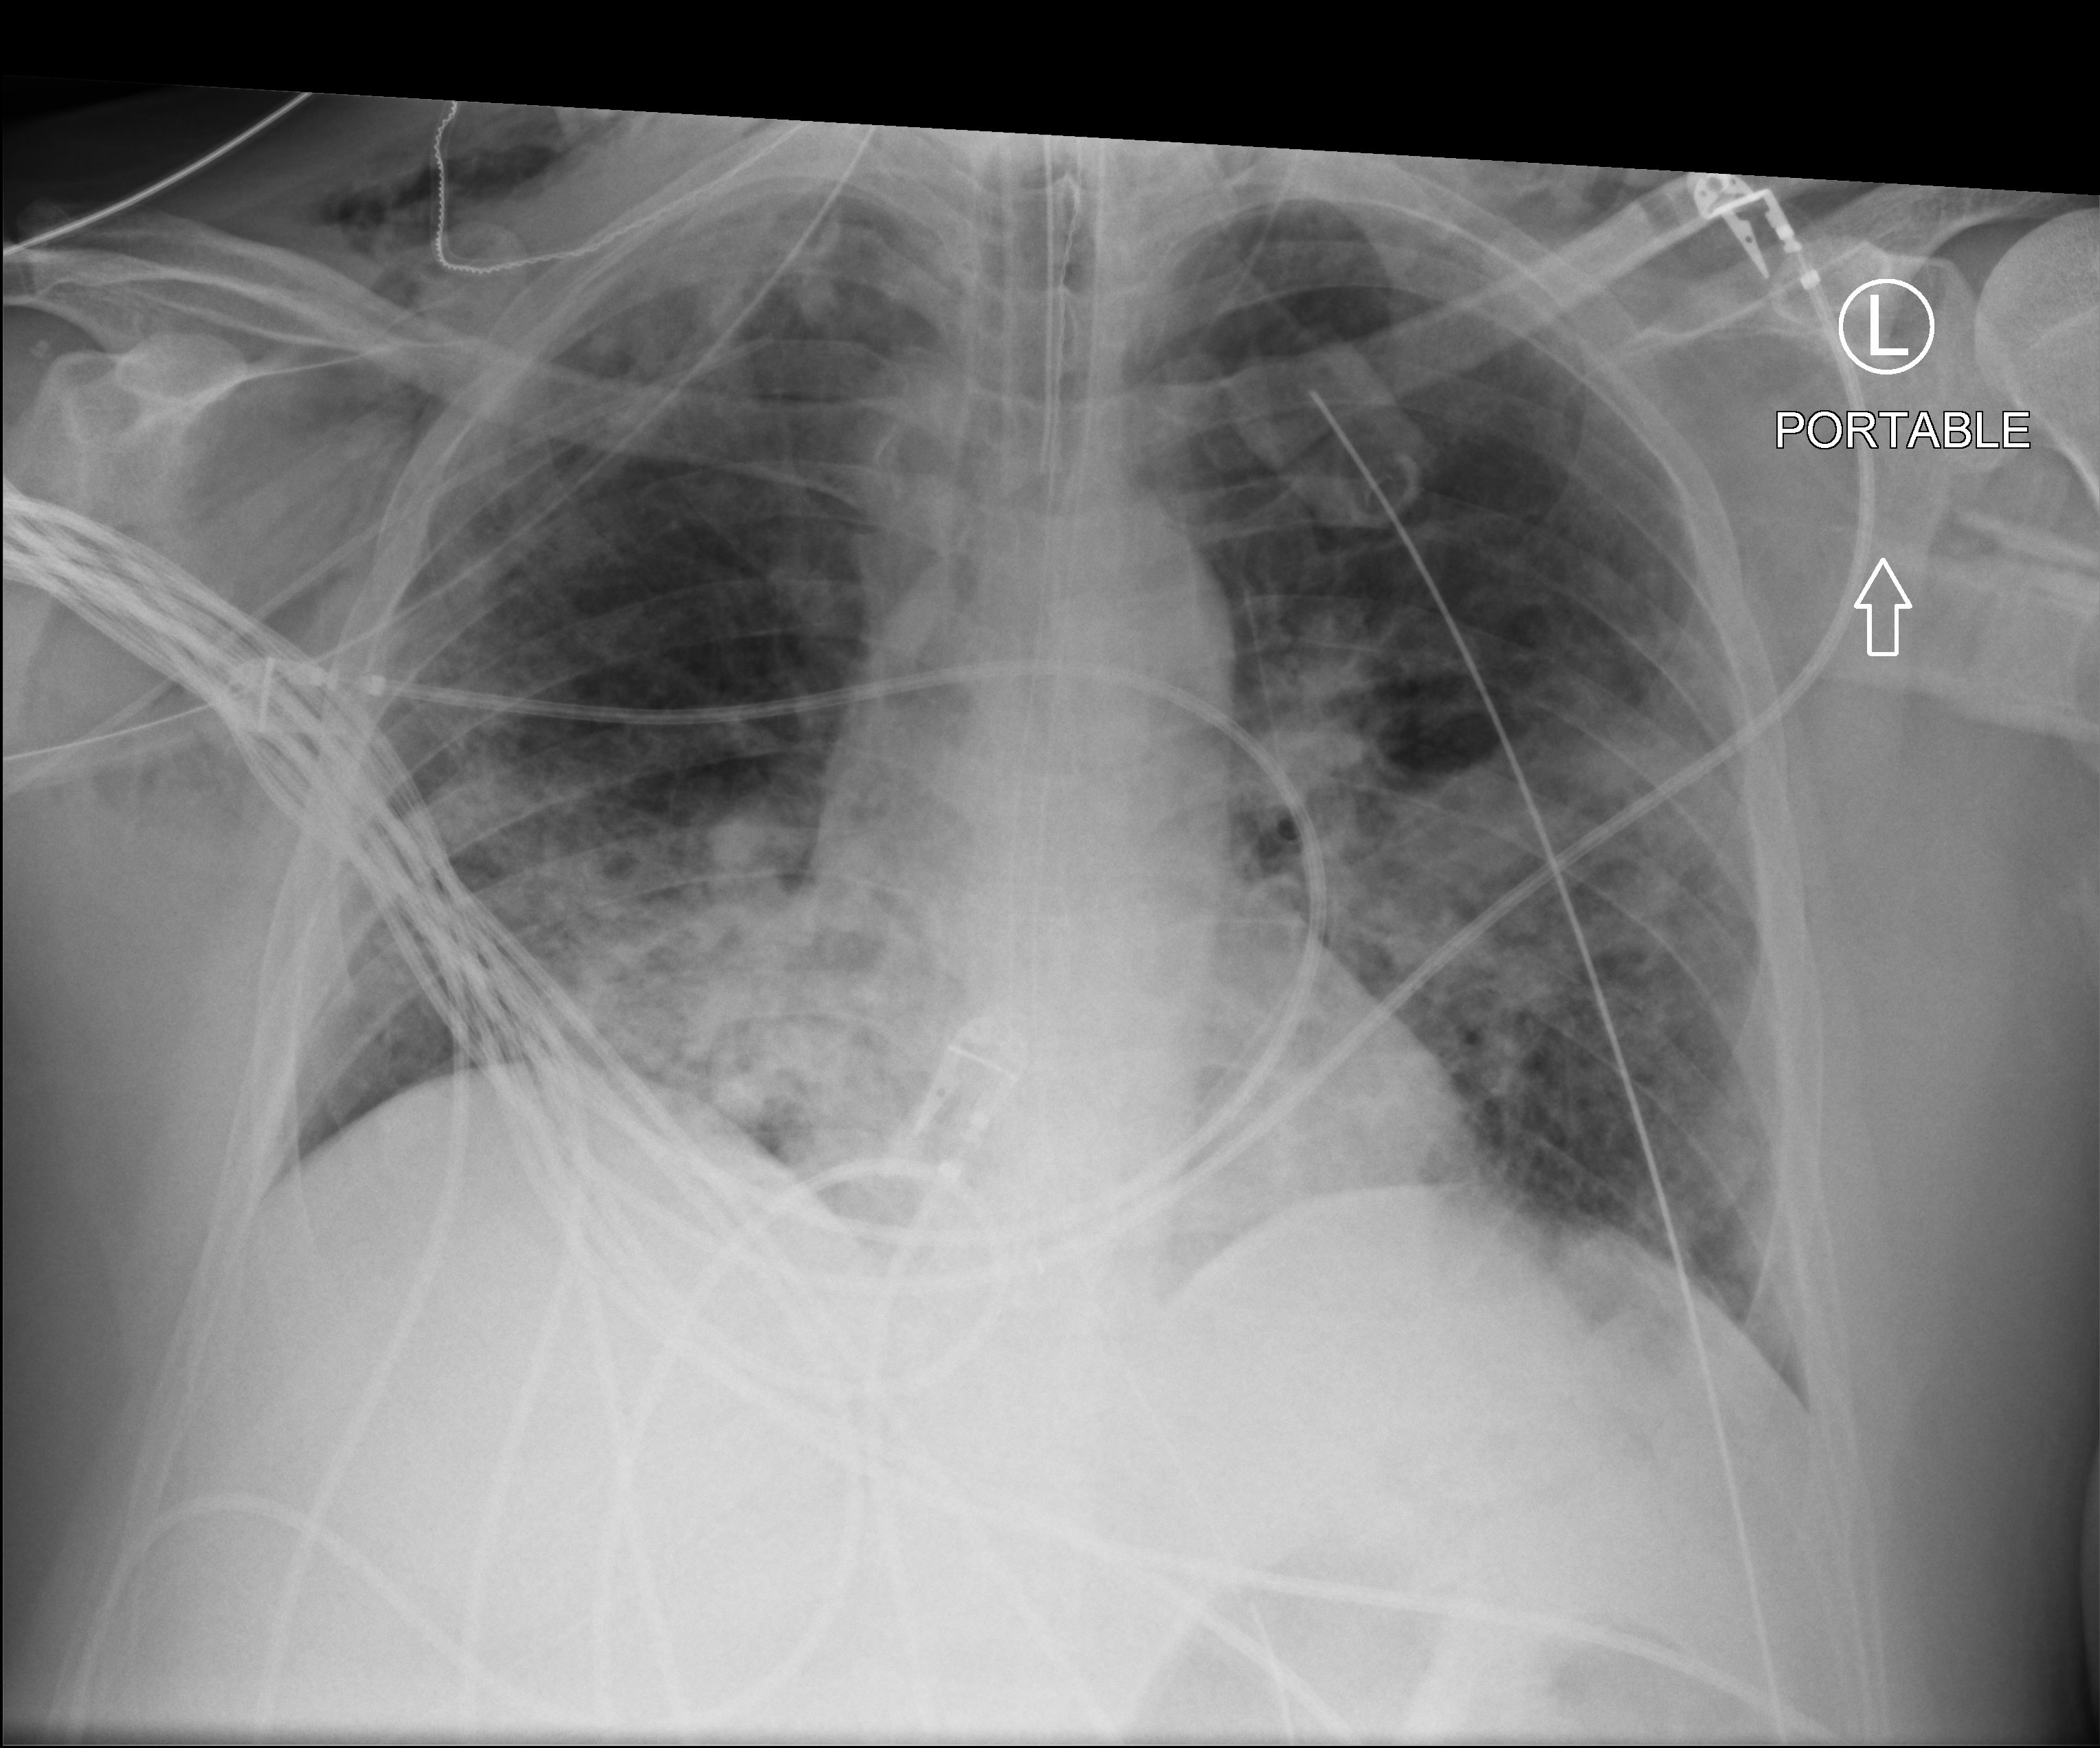
Portable chest radiograph; anteroposterior (AP) projection. Adult patient hospitalised with COVID-19, age 18–59 years.
From the hospital-stay record, not from the radiograph (when in the stay this image was taken is not recorded): mechanically ventilated during this hospital stay: yes.